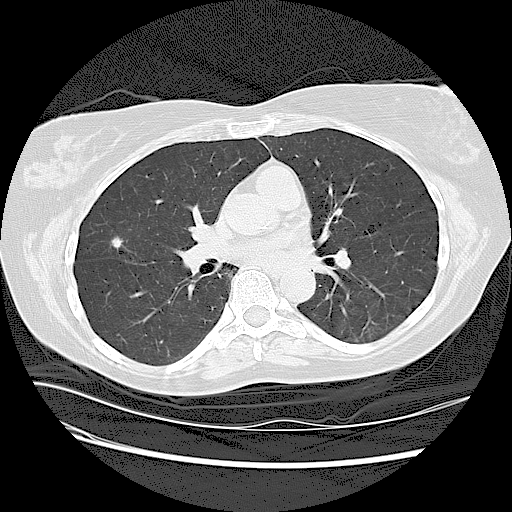
Low-dose screening chest CT, one axial slice; position 63 of 125 along the scan axis; 120 kVp; lung window (W 1500 / L -600 HU); 2.5 mm slice thickness; 512 × 512 image matrix, field of view 360 × 360 mm.
Annotated regions visible in this slice (manually delineated by an expert):
- lesion 1 (tumor, upper lobe of right lung): bounding box [x1, y1, x2, y2] px = [111, 236, 127, 250]